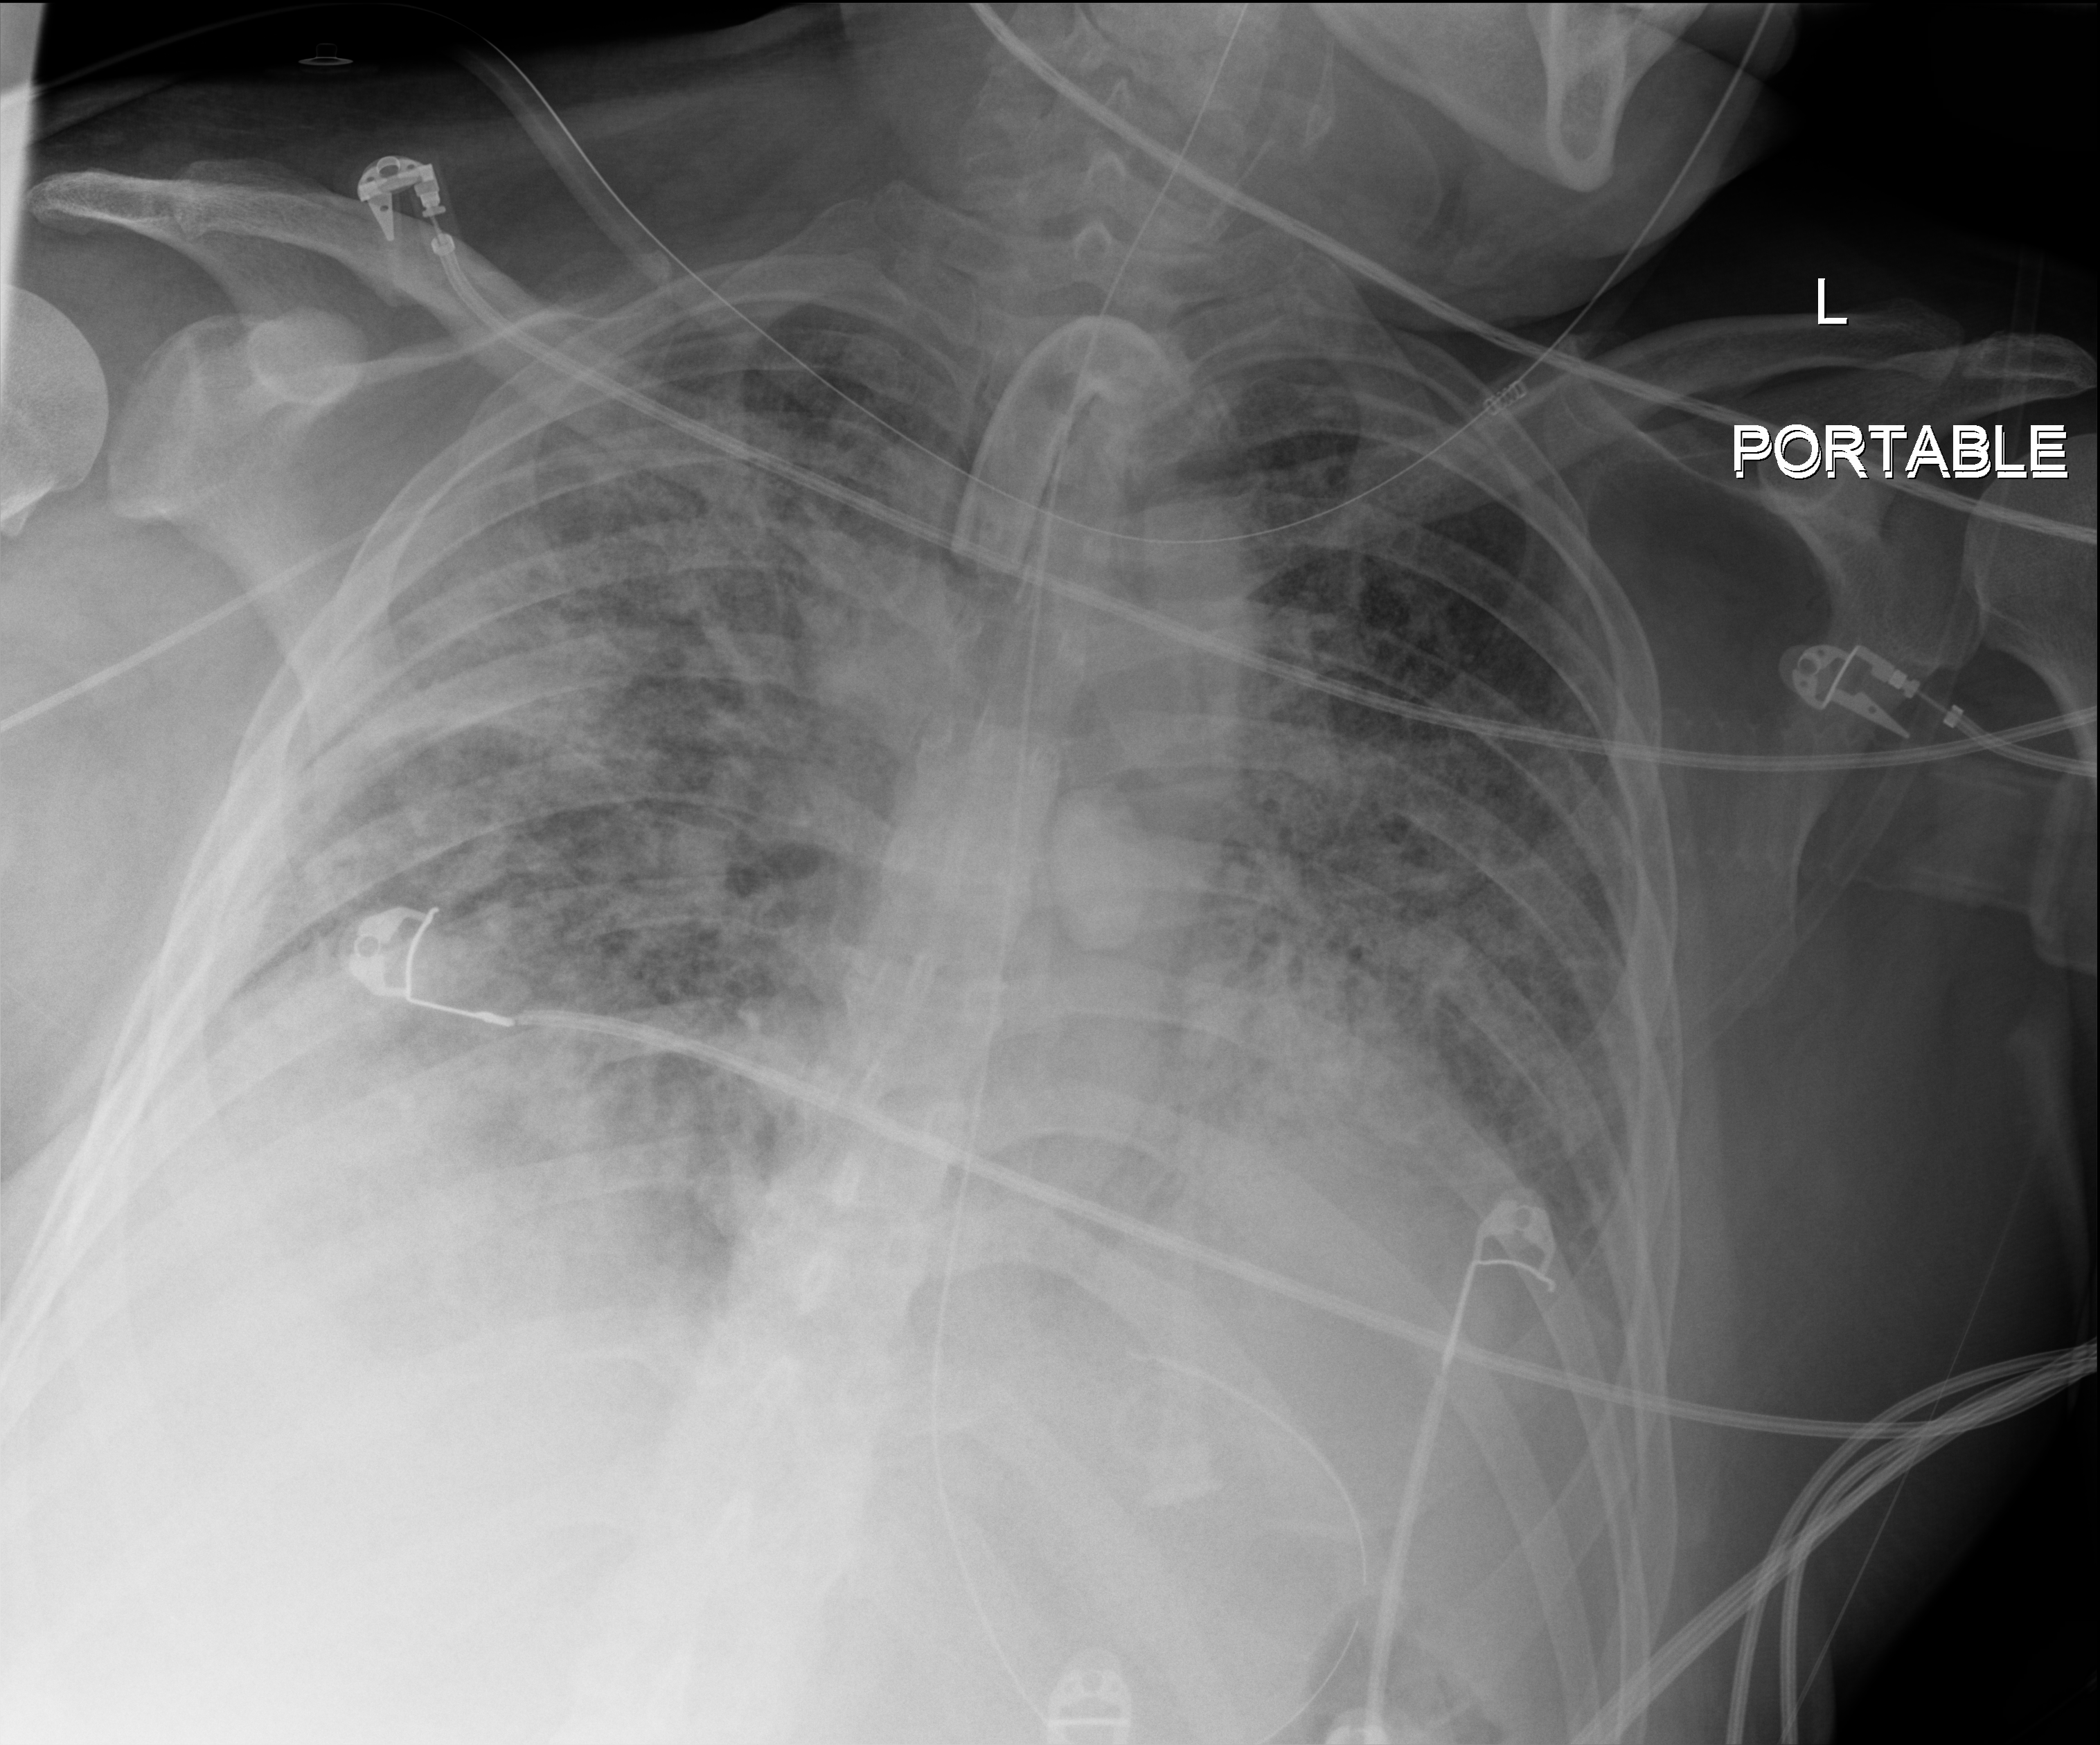
Portable chest radiograph, anteroposterior (AP) projection. Patient hospitalised with COVID-19; male, aged 18–59 years.
From the hospital-stay record, not from the radiograph (when in the stay this image was taken is not recorded): mechanically ventilated during this hospital stay: yes; hypertension (admission record): no; admitted to intensive care during this hospital stay: yes.